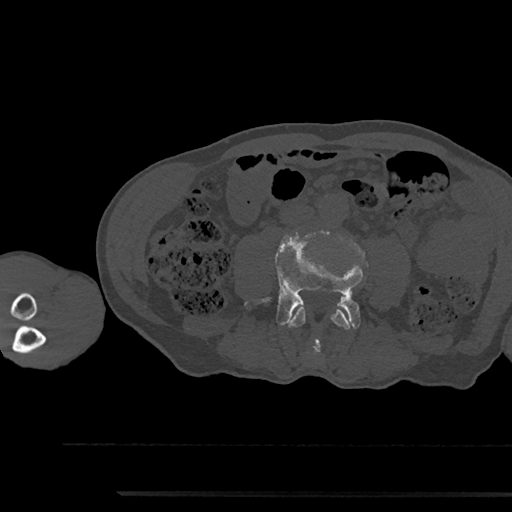
CT including the spine, one axial slice; slice 439 of 797 in the series (ordered by position); 120 kVp; bone window (W 1800 / L 400 HU); 0.5 mm slice thickness; 512 × 512 image matrix, field of view 367 × 367 mm. Patient: male, 79 years. Case-level facts recorded for this patient, not image findings: primary cancer: prostate.
Structures marked on this image (semi-automatically segmented with operator editing):
- L3 vertebra: box from (x=288, y=305) to (x=351, y=353) px
- L4 vertebra: (x=245, y=235)–(x=363, y=348)